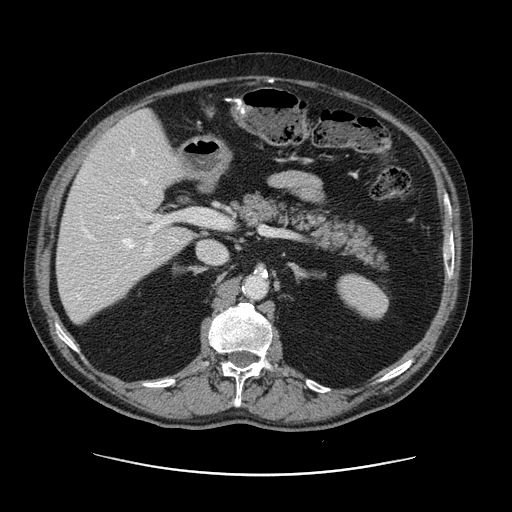
Contrast-enhanced abdominal CT, one axial slice. Position 70 of 141 along the scan axis. 120 kVp. Intravenous contrast given. Soft-tissue window (W 400 / L 40 HU). 2.5 mm slice thickness. 512 × 512 image matrix. Male patient, age 72 years. From the clinical record (not read from this slice): diagnosis: colorectal cancer liver metastases, imaged before liver resection; multiple liver metastases: yes; largest metastasis: 5.4 cm.
Outlined on this slice (expert manual segmentation):
- hepatic veins: box from (x=88, y=148) to (x=147, y=248) px
- liver: (x=57, y=111)–(x=192, y=323)
- planned liver remnant (the part of the liver to remain after resection): (x=57, y=186)–(x=193, y=323)
- portal vein (with intrahepatic branches): (x=76, y=198)–(x=203, y=299)